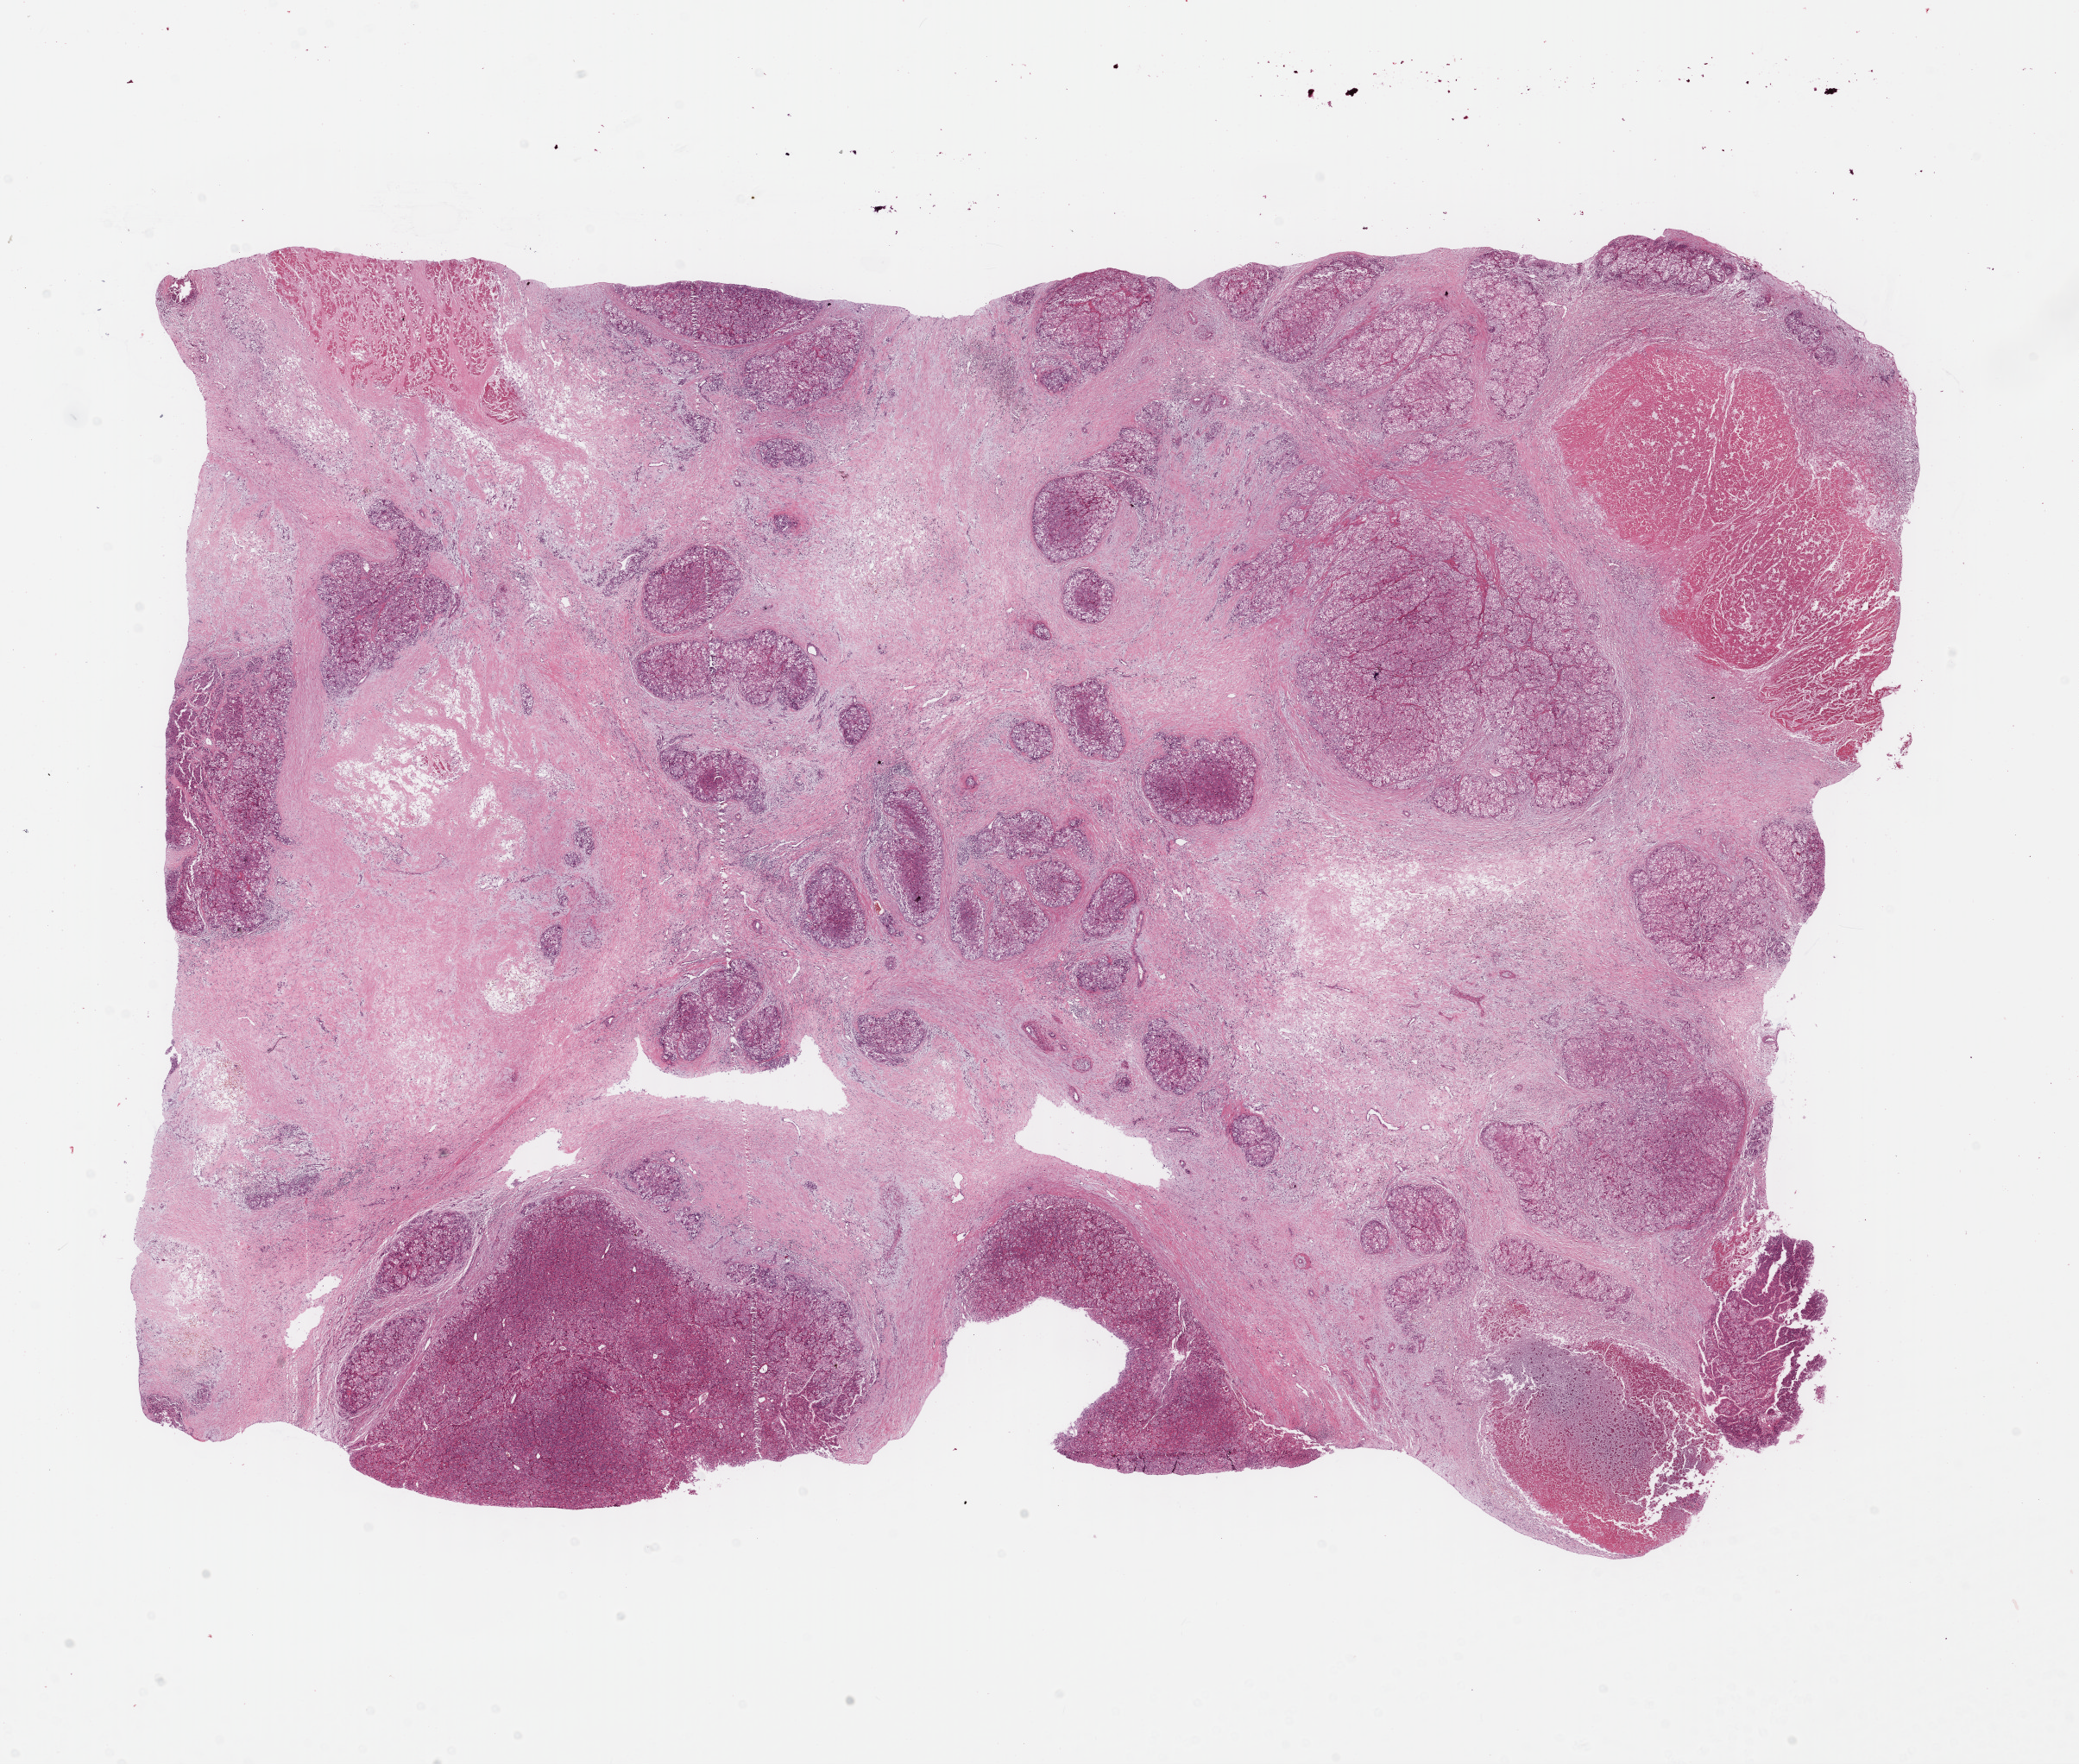
Whole-slide histology image, H&E-stained — low-resolution overview of the scanned area, about 18.9 x 16.1 mm, formalin-fixed paraffin-embedded (FFPE) diagnostic section, primary tumour sample from the liver. Male patient; age at initial diagnosis 54 years.
Histologic diagnosis: Hepatocellular carcinoma, NOS.